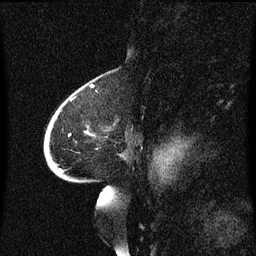
Breast MRI (dynamic contrast-enhanced), one sagittal slice. Position 42 of 60 along the scan axis. Dynamic contrast-enhanced series, image 2 of 3 at this slice position (ordered by acquisition). 1.5 T. TE 4.2 ms, TR 8.4 ms. 2 mm slice thickness. 256 × 256 image matrix, field of view 200 × 200 mm. Female patient, age 68 years. Case-level facts recorded for this patient, not image findings: setting: breast cancer imaged before/during neoadjuvant chemotherapy; receptor status: triple-negative.
Outlined on this slice (semi-automatic segmentation, software-assisted and operator-edited):
- analysis volume of interest (the breast-tissue region the enhancement analysis was run in; not a lesion): box from (x=45, y=94) to (x=125, y=173) px
- tumour enhancement mask (voxels above the 70 % enhancement threshold inside the analysis volume of interest): (x=60, y=170)–(x=63, y=173)